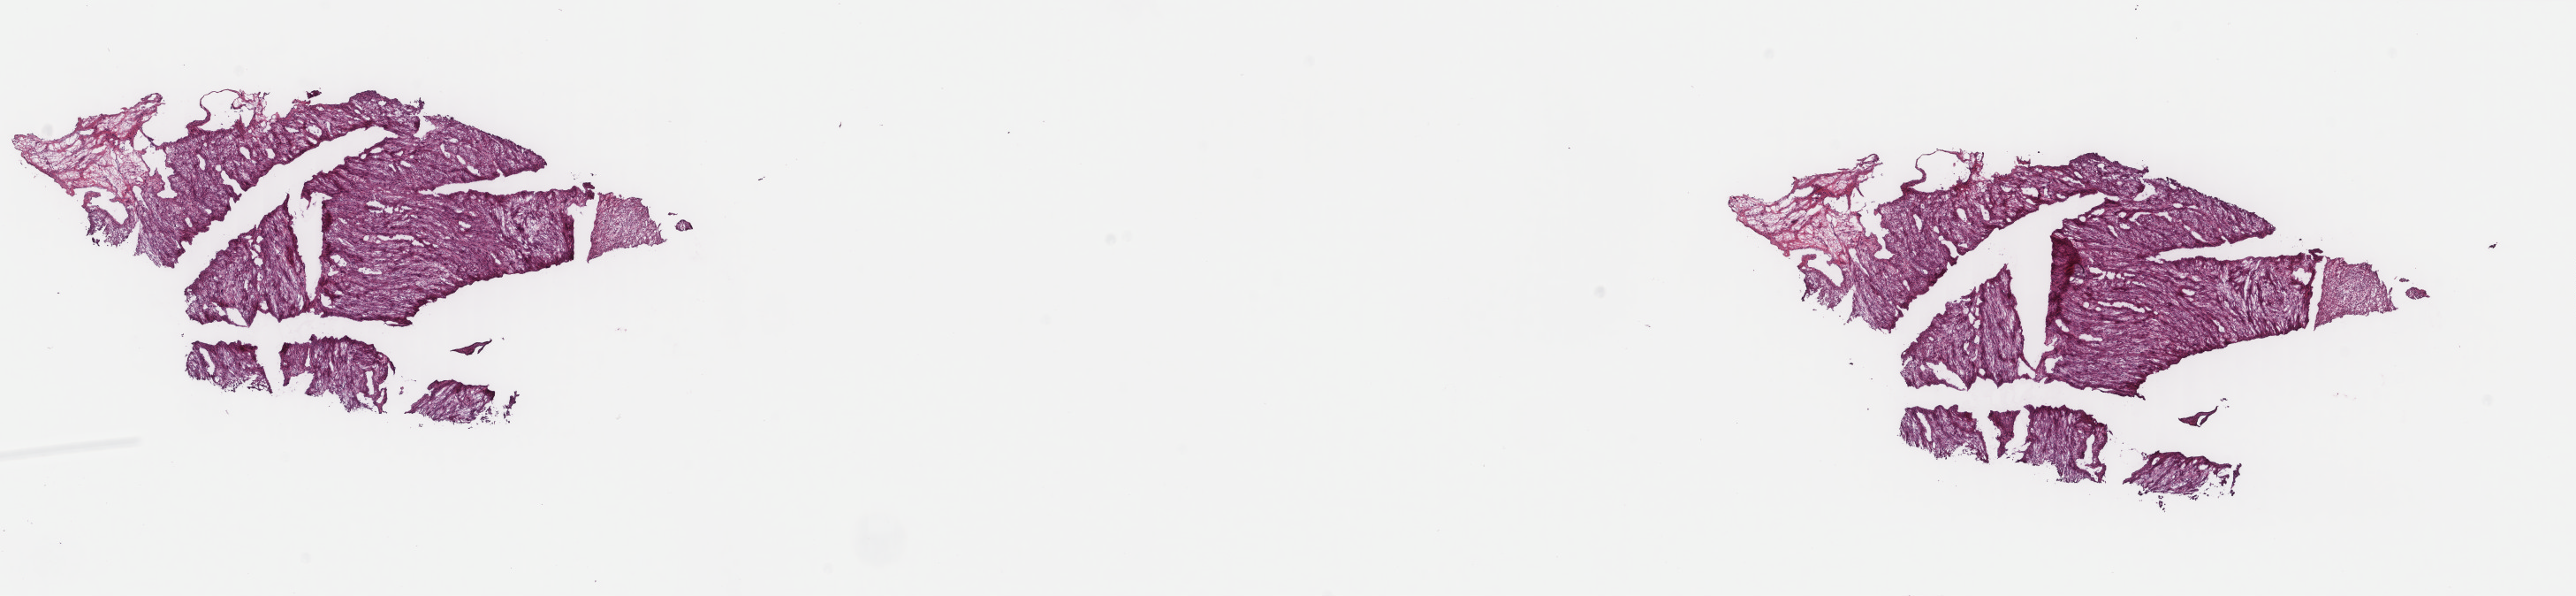
Digitized H&E-stained tissue section (whole slide), shown as a low-resolution overview of the whole scanned area (about 23.1 x 5.3 mm); frozen section from the top of the tissue portion; connective, subcutaneous and other soft tissues, primary tumour sample. Female patient; age at initial diagnosis 66 years. Pathologist review of this section (percent, as recorded): tumour cells 100%, tumour nuclei 92%.
Histologic diagnosis: Leiomyosarcoma, NOS (connective, subcutaneous and other soft tissues of trunk, NOS).